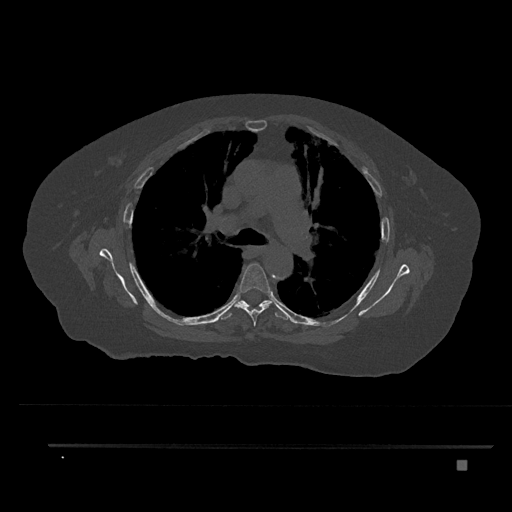
CT including the spine, one axial slice; slice 554 of 797 in the series (ordered by position); 120 kVp; bone window (W 1800 / L 400 HU); 512 × 512 image matrix, field of view 437 × 437 mm. Female patient, age 76 years. From the clinical record (not read from this slice): primary cancer: lung; vertebrae with lytic lesions (as recorded): T11, L3.
Structures marked on this image (semi-automatically segmented with operator editing):
- T5 vertebra: bounding box [x1, y1, x2, y2] px = [234, 263, 274, 326]
- T6 vertebra: [219, 300, 290, 320]